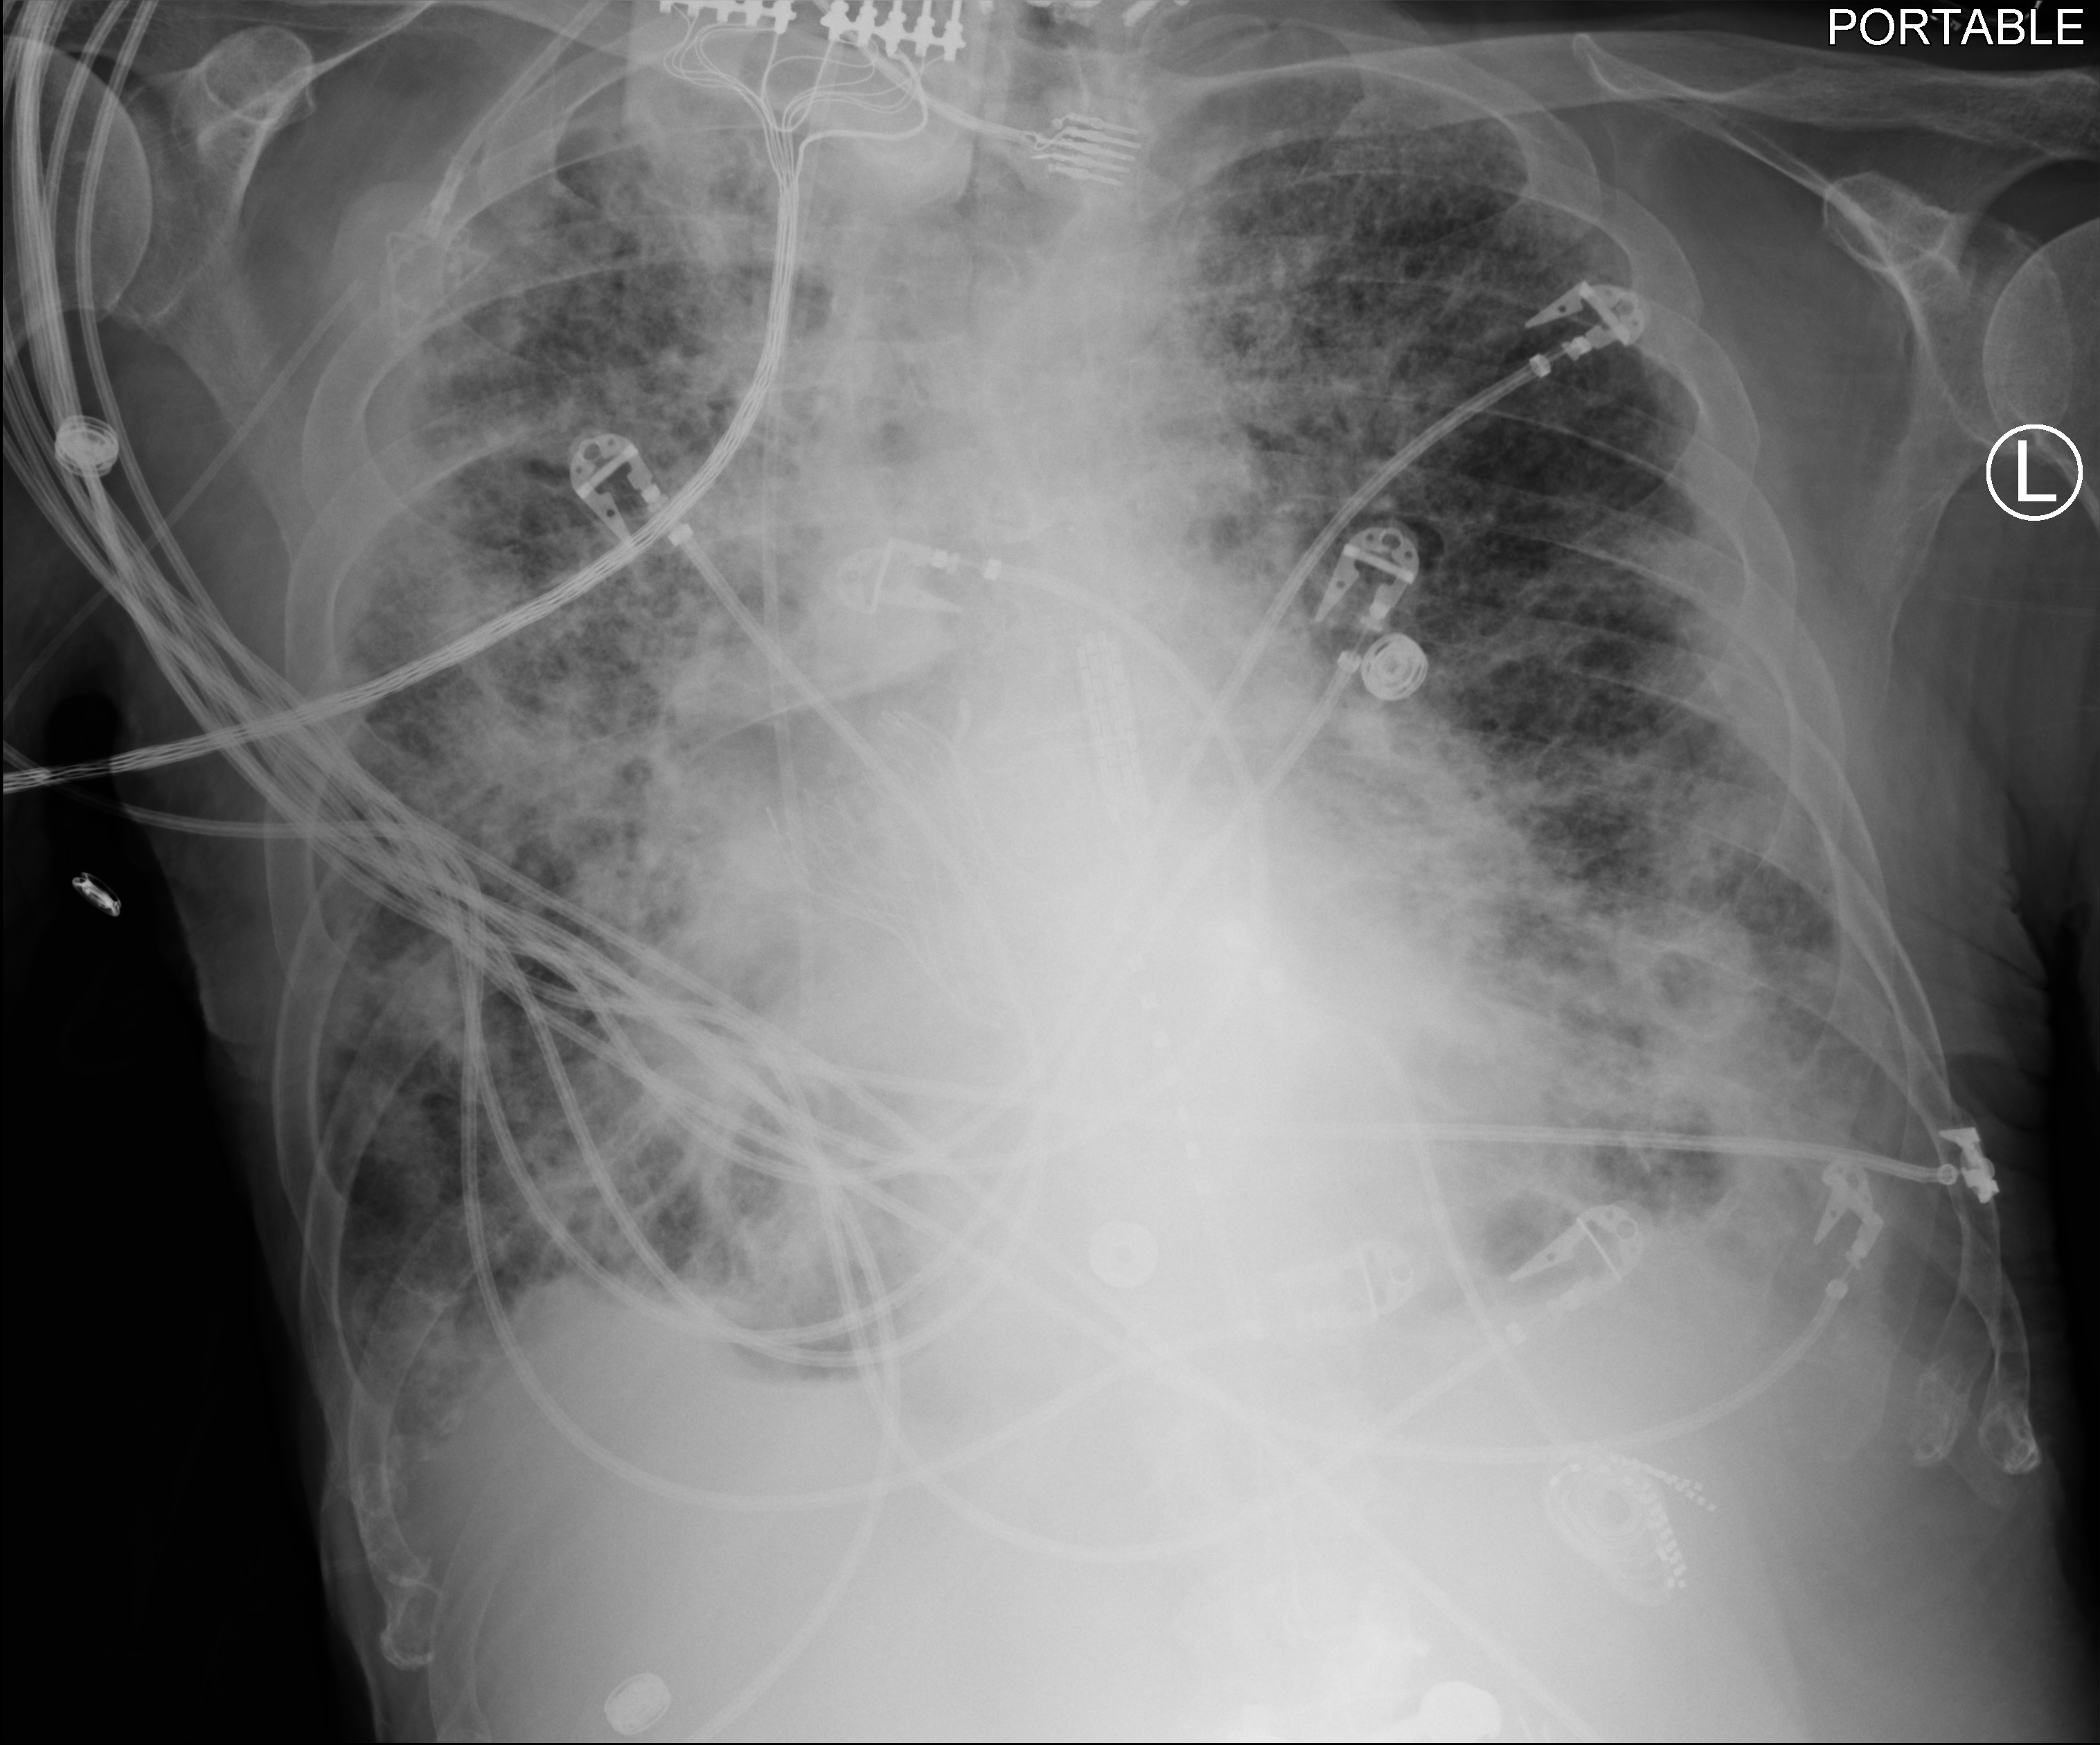
Bedside chest radiograph (computed radiography), anteroposterior (AP) projection. Male patient hospitalised with COVID-19, age 75–90 years.
From the hospital-stay record, not from the radiograph (when in the stay this image was taken is not recorded): admitted to intensive care during this hospital stay: yes; mechanically ventilated during this hospital stay: no.